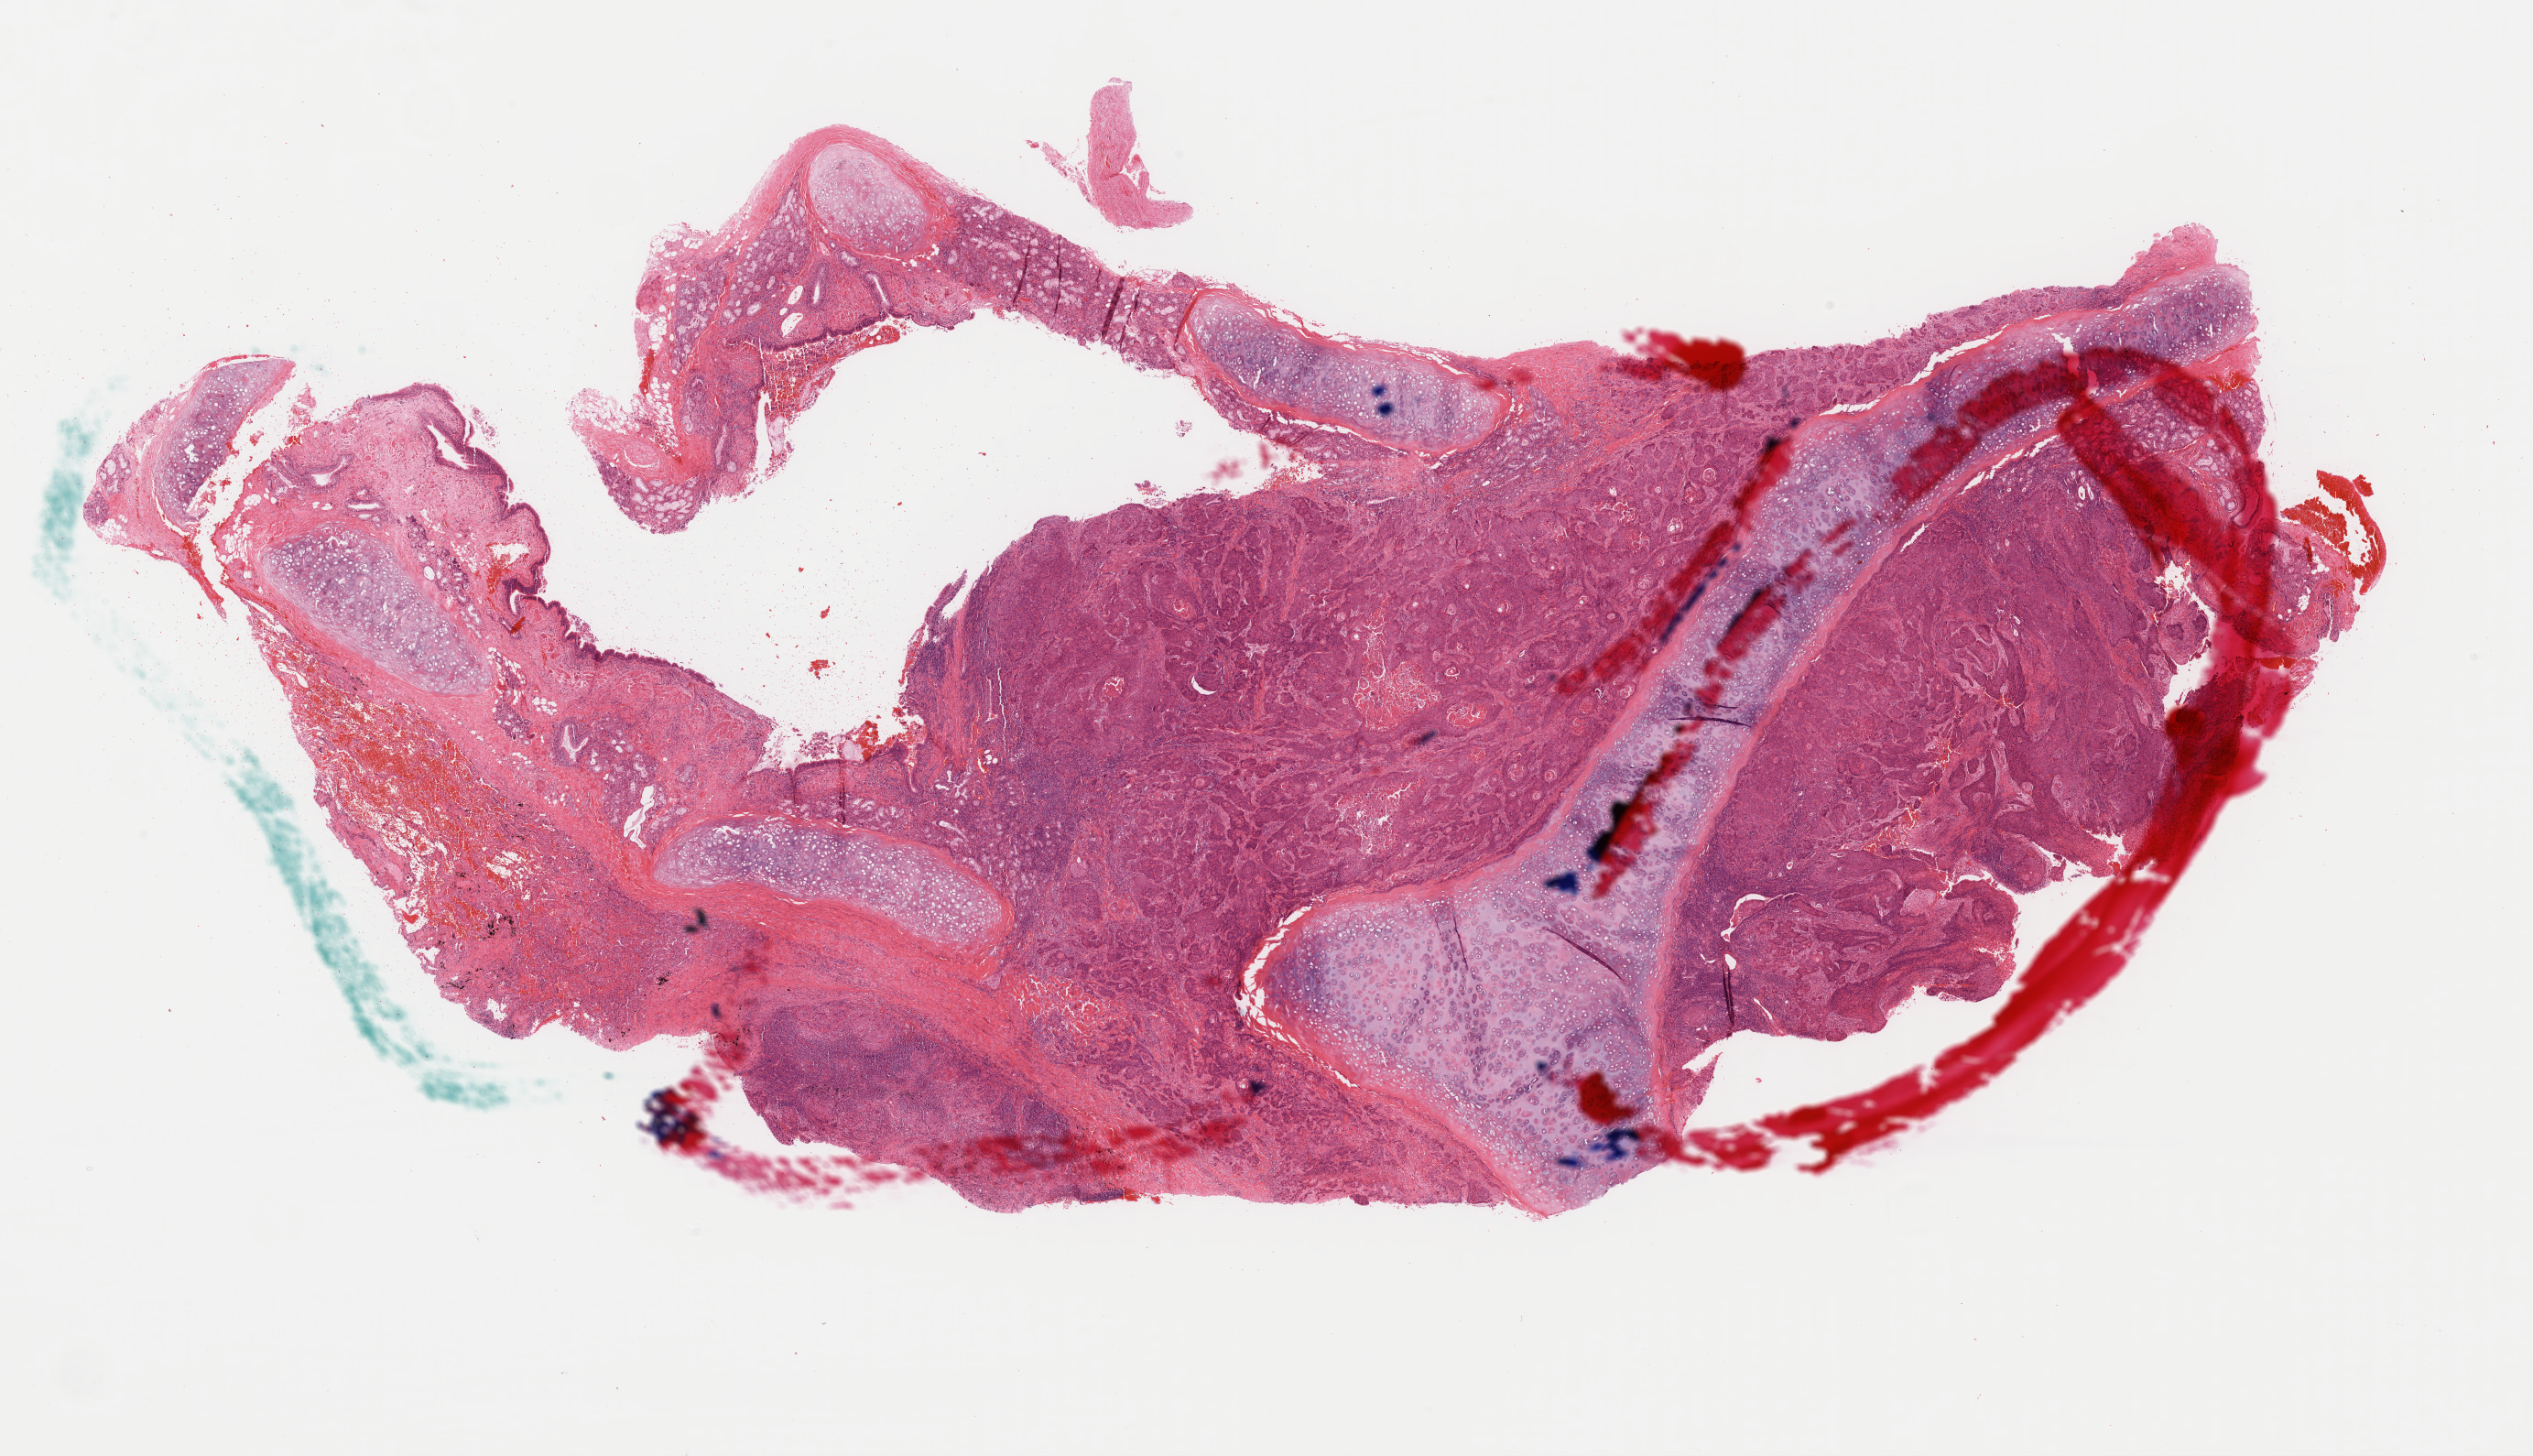
H&E whole-slide image, a low-resolution overview of the entire scanned area, about 21.9 x 12.6 mm (acquisition: 40x scan). Formalin-fixed paraffin-embedded (FFPE) diagnostic section. Lung, primary tumour sample. Patient: male, age at initial diagnosis 68 years.
AJCC pathologic stage: IB (7th edition). Laterality: right. Diagnosis: Squamous cell carcinoma, keratinizing, NOS.